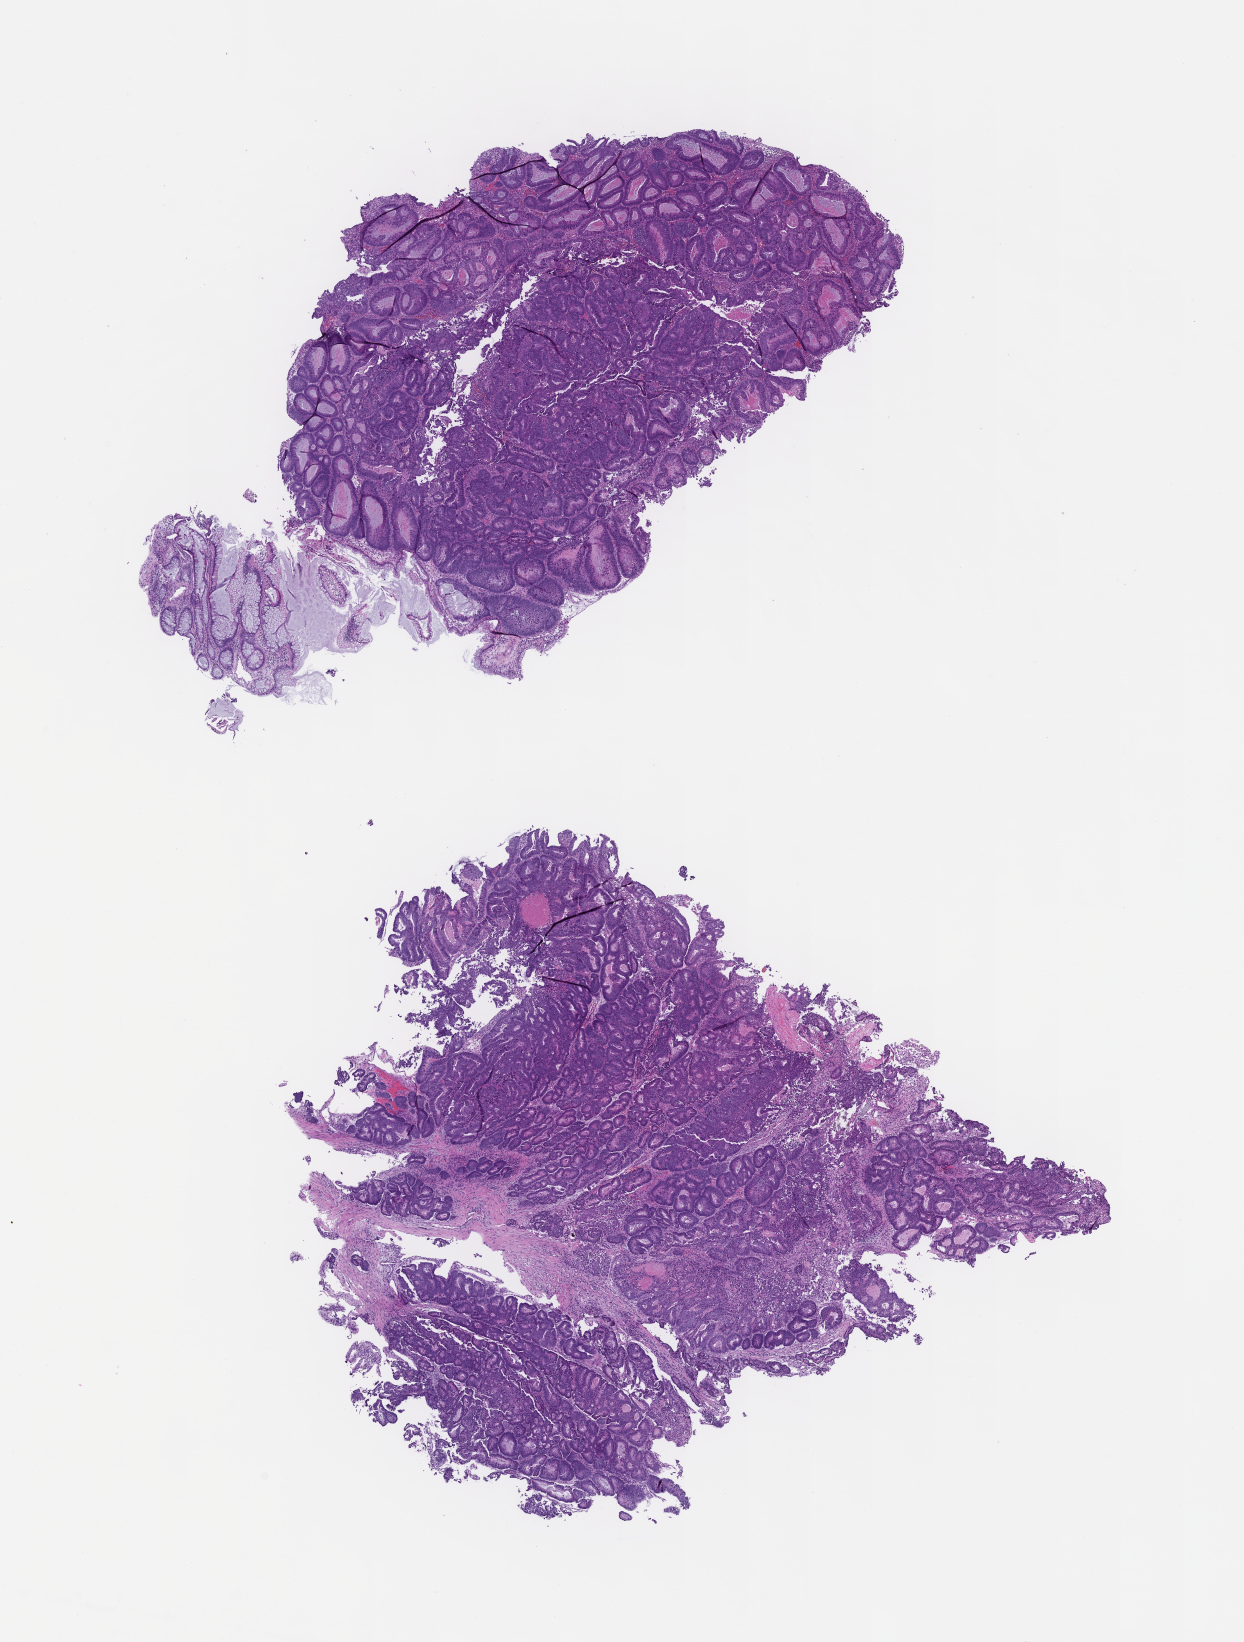
Whole-slide image, hematoxylin and eosin (H&E) stain — whole scanned area (about 10.1 x 13.3 mm) shown as a low-resolution overview. FFPE section. Tissue site: colon. Specimen time point: archival tissue. Male patient.
* this section: primary tumor
* diagnosis: Colorectal Carcinoma